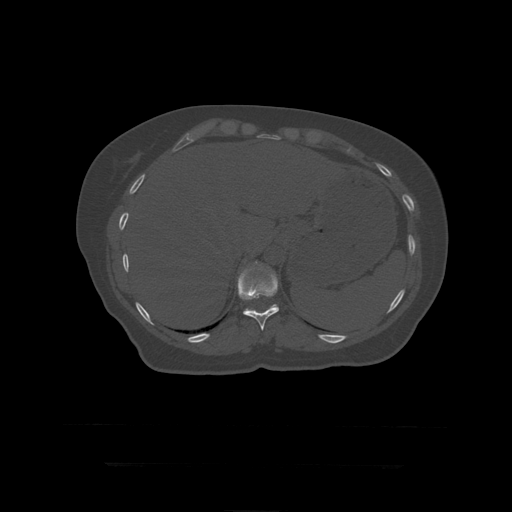
CT including the spine, one axial slice. Position 215 of 399 along the scan axis. Reconstruction kernel STANDARD. 120 kVp. Bone window (W 1800 / L 400 HU). 1.25 mm slice thickness. 512 × 512 image matrix, field of view 450 × 450 mm. Patient age 41 years. Case-level facts recorded for this patient, not image findings: primary cancer: breast.
Structures marked on this image (semi-automatic segmentation, software-assisted and operator-edited):
- T11 vertebra: bounding box <238,263,279,331> (left, top, right, bottom; pixels)
- T12 vertebra: <243,262,279,313>